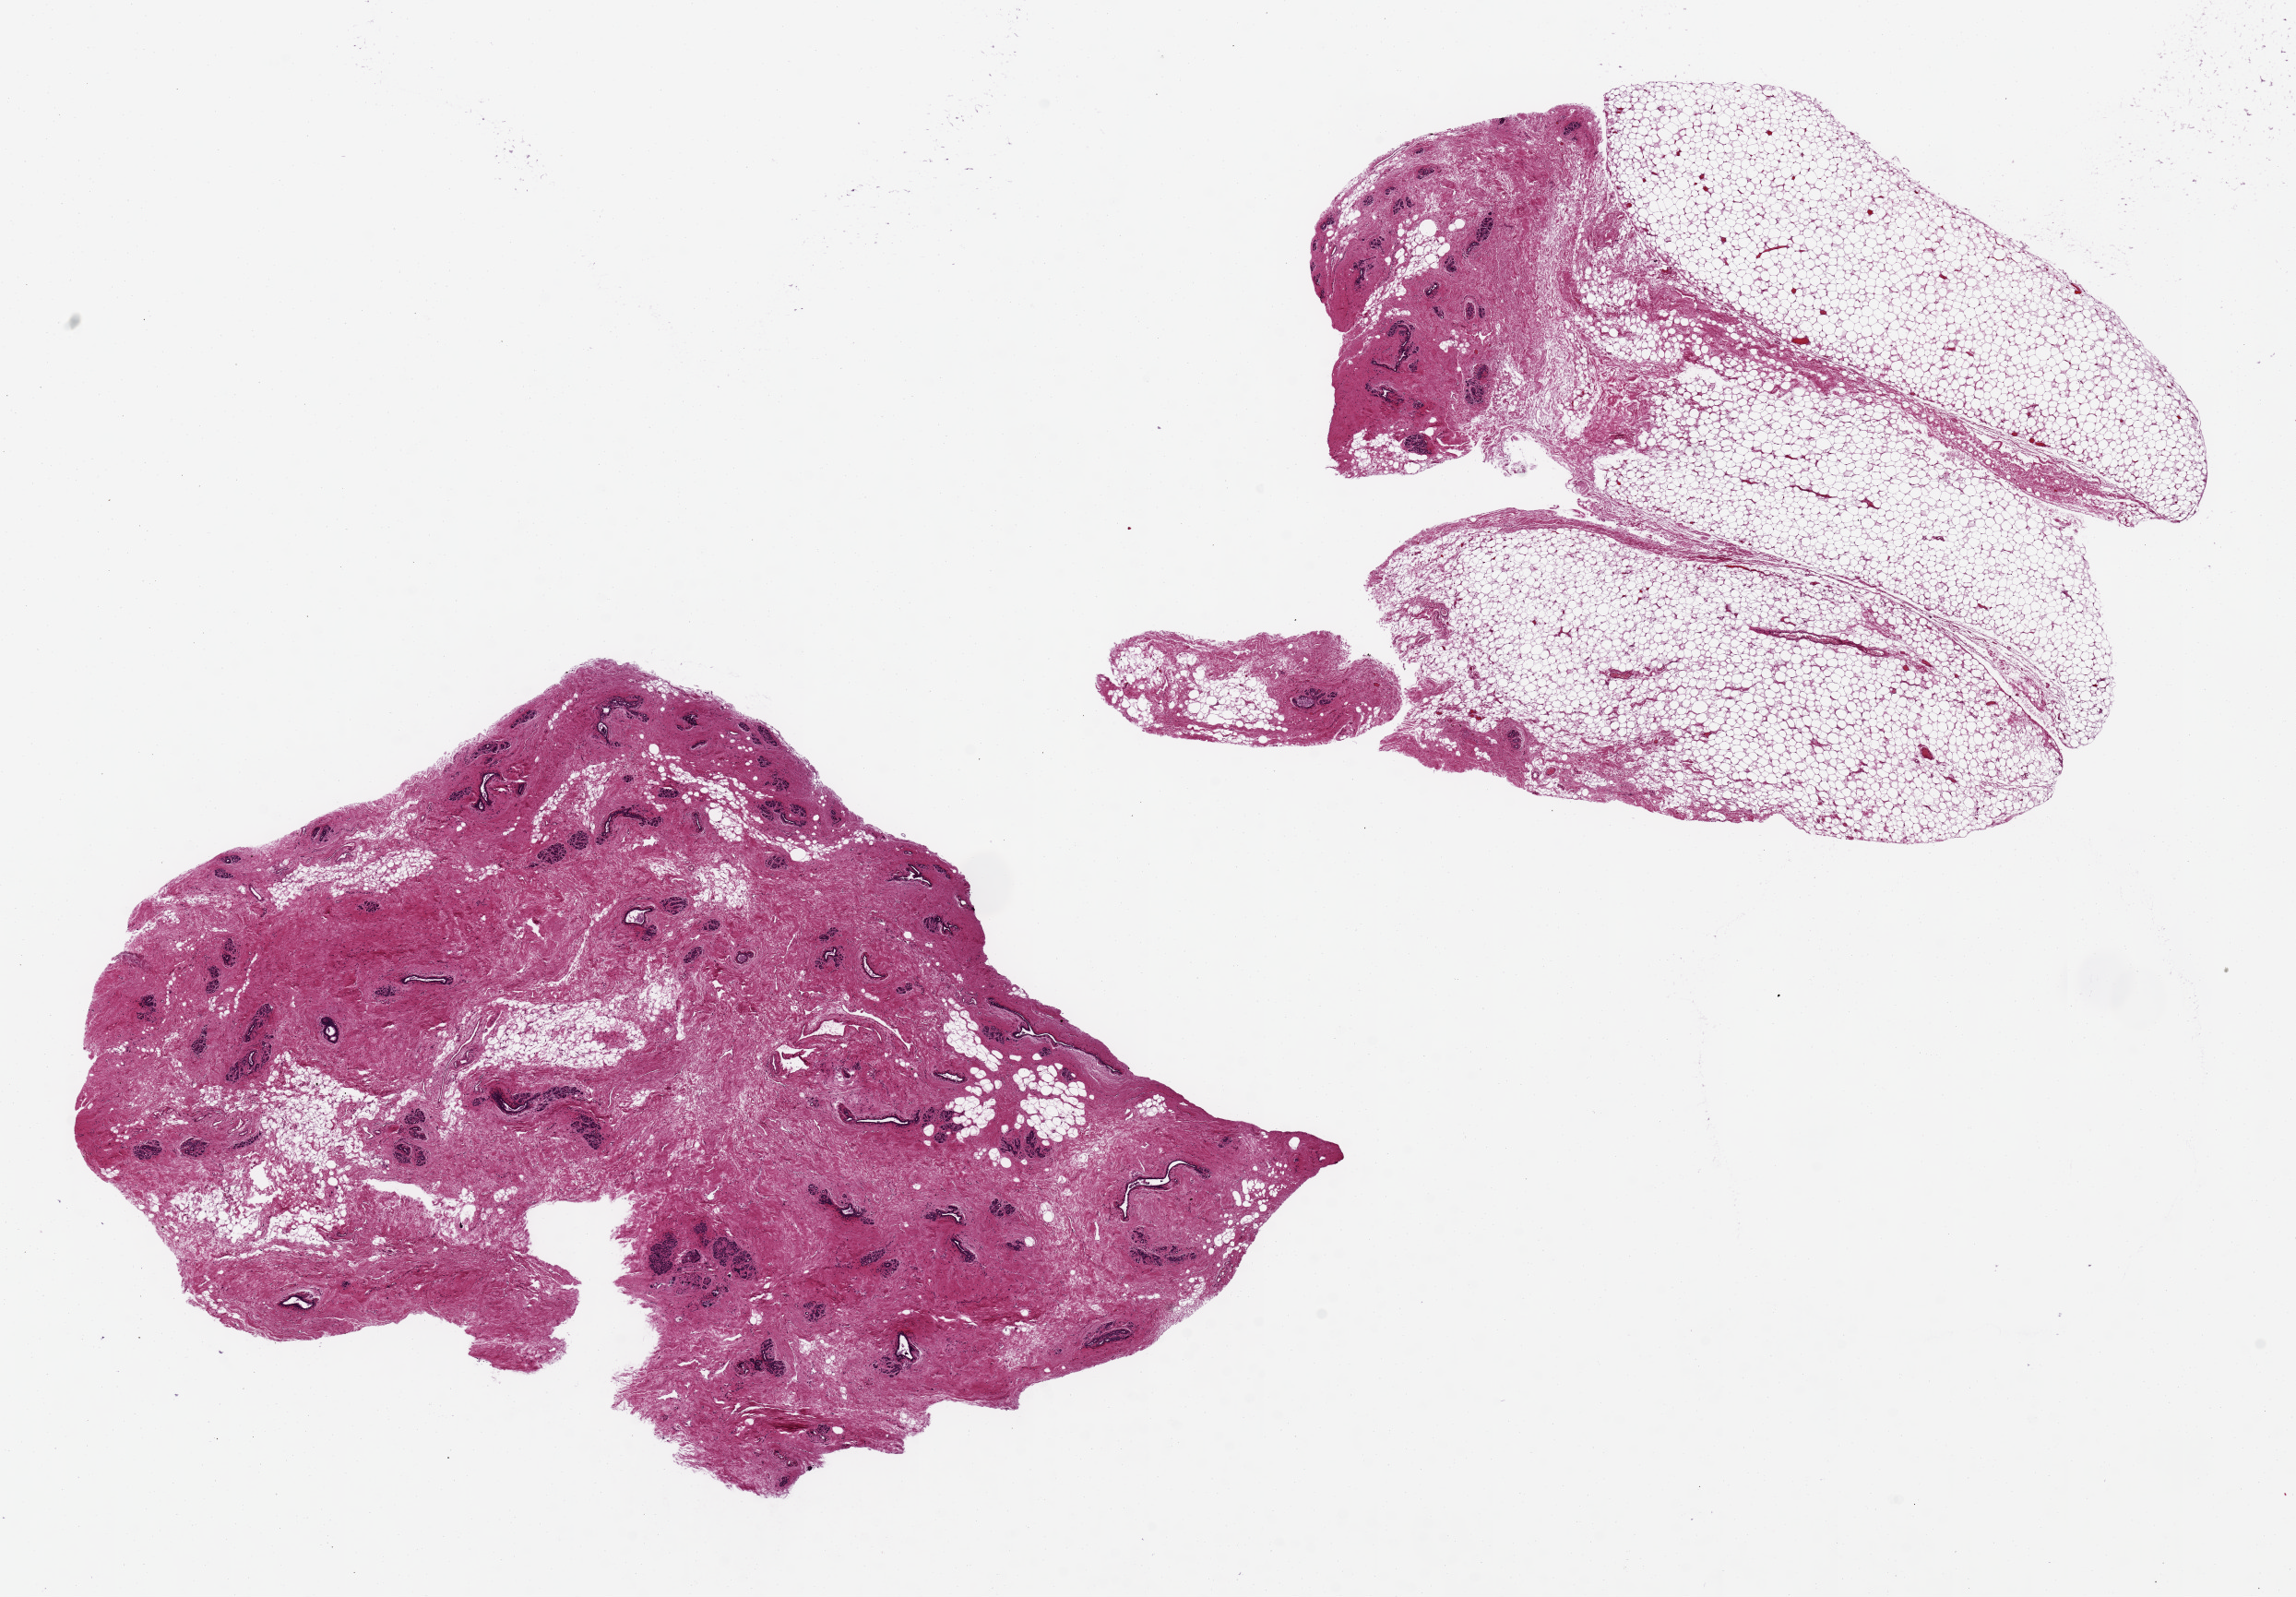
Whole-slide image, haematoxylin and eosin stain, brightfield — a low-resolution overview of the entire scanned area, about 19.7 x 13.7 mm (from a 20x scan). PAXgene-fixed, paraffin-embedded tissue. Section of breast (target tissue). Tissue donor sample. Female donor.
Pathologist's review note for this sample: 2 pieces 7x7 & 7x6 mm; 1 piece has 90% adjacent adipose tissue; other has ducts and lobules with ~20% admixed adipose tissue.